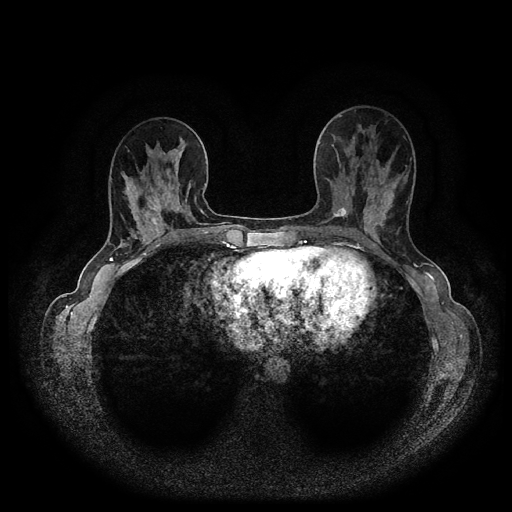
Breast MRI (dynamic contrast-enhanced, multi-phase), one axial slice. Position 38 of 116 along the scan axis. Dynamic contrast-enhanced series, time point 2 of 5 at this slice position (early post-contrast). 1.5 T. TE 2.6 ms, TR 5.4 ms. 2 mm slice thickness. 512 × 512 image matrix, field of view 340 × 340 mm. Patient: female, 40 years.
Annotated regions visible in this slice (semi-automatically segmented with operator editing):
- breast lesion (labelled 'tumour' in the annotation; benign lesions carry a separate 'benign' label): bounding box [x1, y1, x2, y2] px = [332, 205, 349, 219]